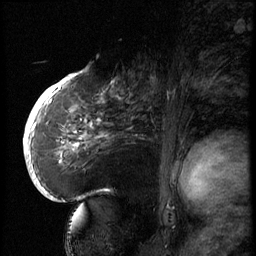
Breast MRI (dynamic contrast-enhanced), one sagittal slice; position 36 of 66 along the scan axis; 3 images stored at this slice position (order not interpretable as contrast timing); 1.5 T; TE 4.2 ms, TR 8.9 ms; 256 × 256 image matrix. Female patient, age 56 years. Case-level facts recorded for this patient, not image findings: setting: breast cancer imaged before/during neoadjuvant chemotherapy.
Outlined on this slice (semi-automatically segmented with operator editing):
- analysis volume of interest (the breast-tissue region the enhancement analysis was run in; not a lesion): bounding box (x1, y1, x2, y2) in pixels: (129, 62, 194, 127)
- tumour enhancement mask (voxels above the 140 % enhancement threshold inside the analysis volume of interest): (152, 77, 170, 97)